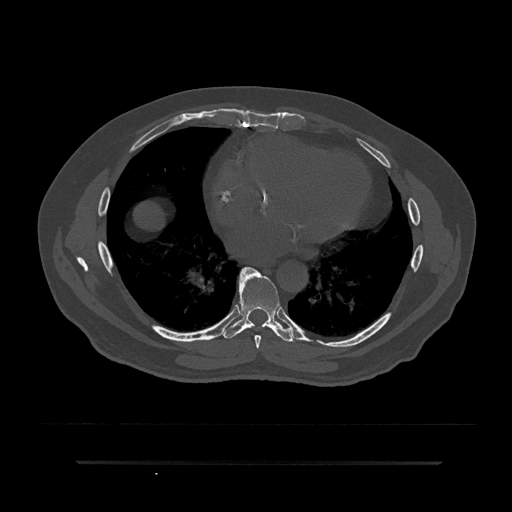
CT including the spine, one axial slice; slice 446 of 797 in the series (ordered by position); reconstruction kernel Br40s/3; 120 kVp; bone window (W 1800 / L 400 HU); 0.5 mm slice thickness; 512 × 512 image matrix, field of view 464 × 464 mm. Patient: male, 59 years. From the clinical record (not read from this slice): primary cancer: bile ducts; vertebrae with lytic lesions (as recorded): T10.
Structures marked on this image (semi-automatically segmented with operator editing):
- T7 vertebra: box from (x=239, y=267) to (x=261, y=349) px
- T8 vertebra: (x=222, y=270)–(x=295, y=342)